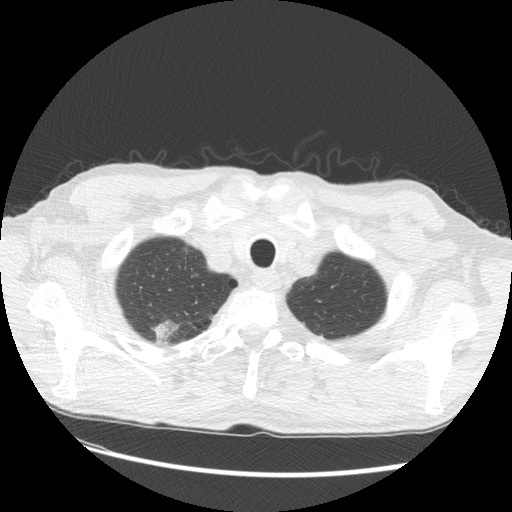
Low-dose screening chest CT, one axial slice. Position 122 of 133 along the scan axis. 120 kVp. Lung window (W 1500 / L -600 HU). 2.5 mm slice thickness. 512 × 512 image matrix.
Structures marked on this image (expert manual segmentation):
- lesion 2 (tumor, upper lobe of right lung): bounding box <151,319,181,346> (left, top, right, bottom; pixels)